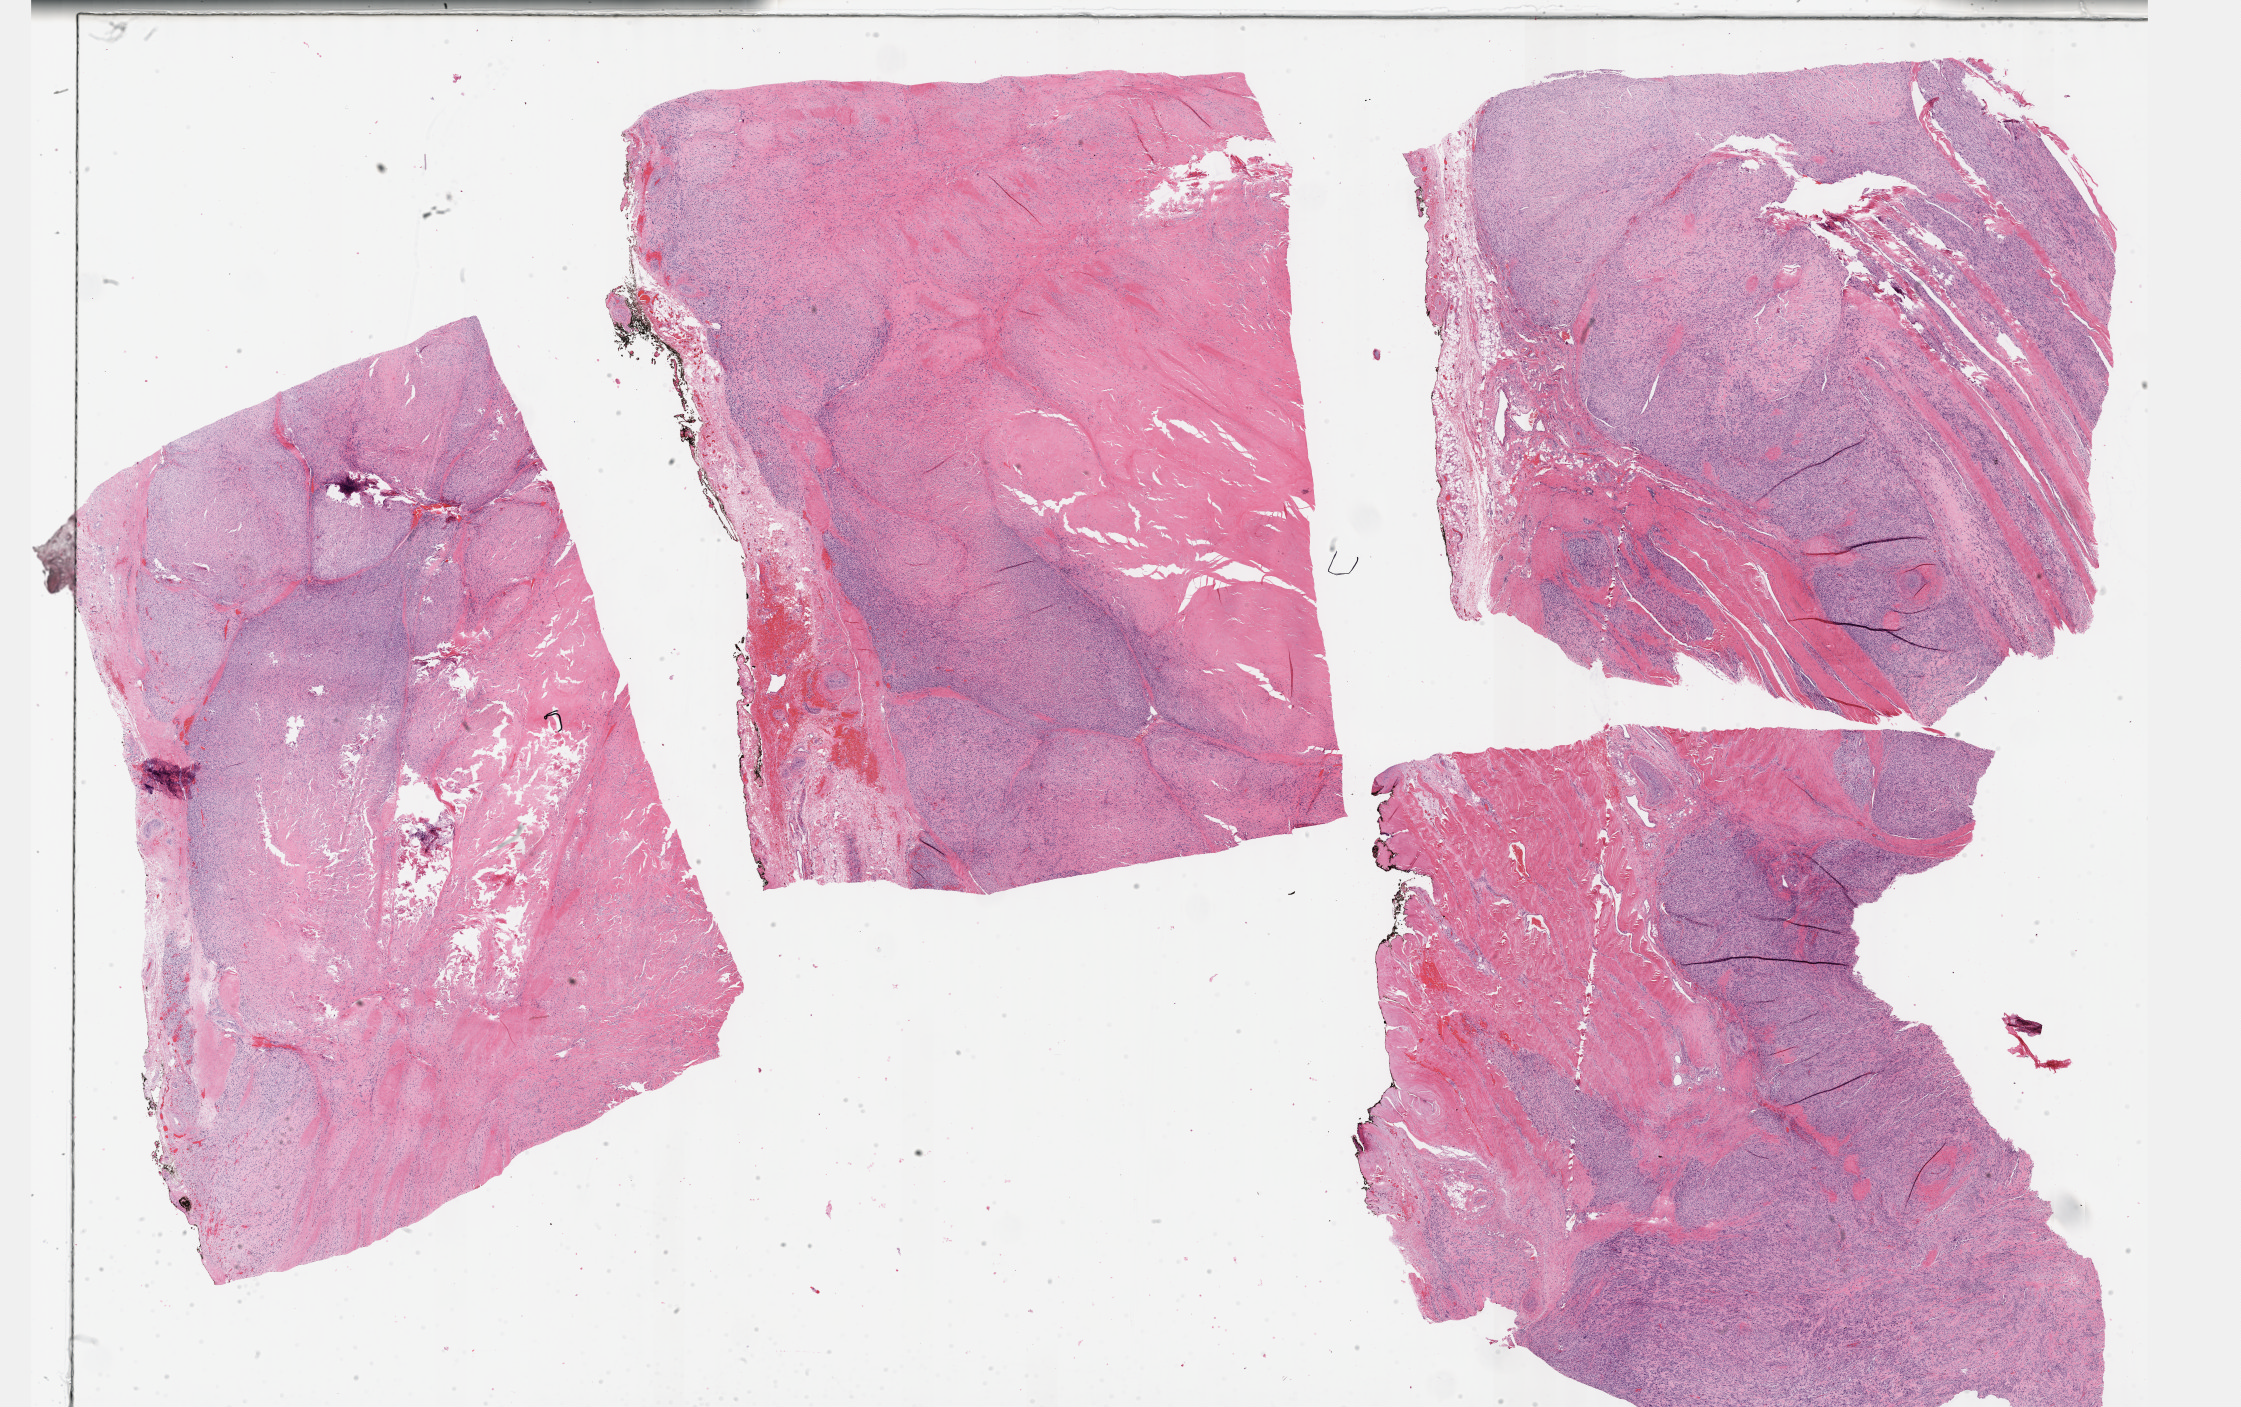
H&E whole-slide image, whole scanned area (about 36.2 x 22.7 mm) shown as a low-resolution overview; formalin-fixed paraffin-embedded (FFPE) diagnostic section; primary tumour sample from the connective, subcutaneous and other soft tissues. Patient: male, age at initial diagnosis 74 years.
Diagnosis: Leiomyosarcoma, NOS (connective, subcutaneous and other soft tissues of lower limb and hip).